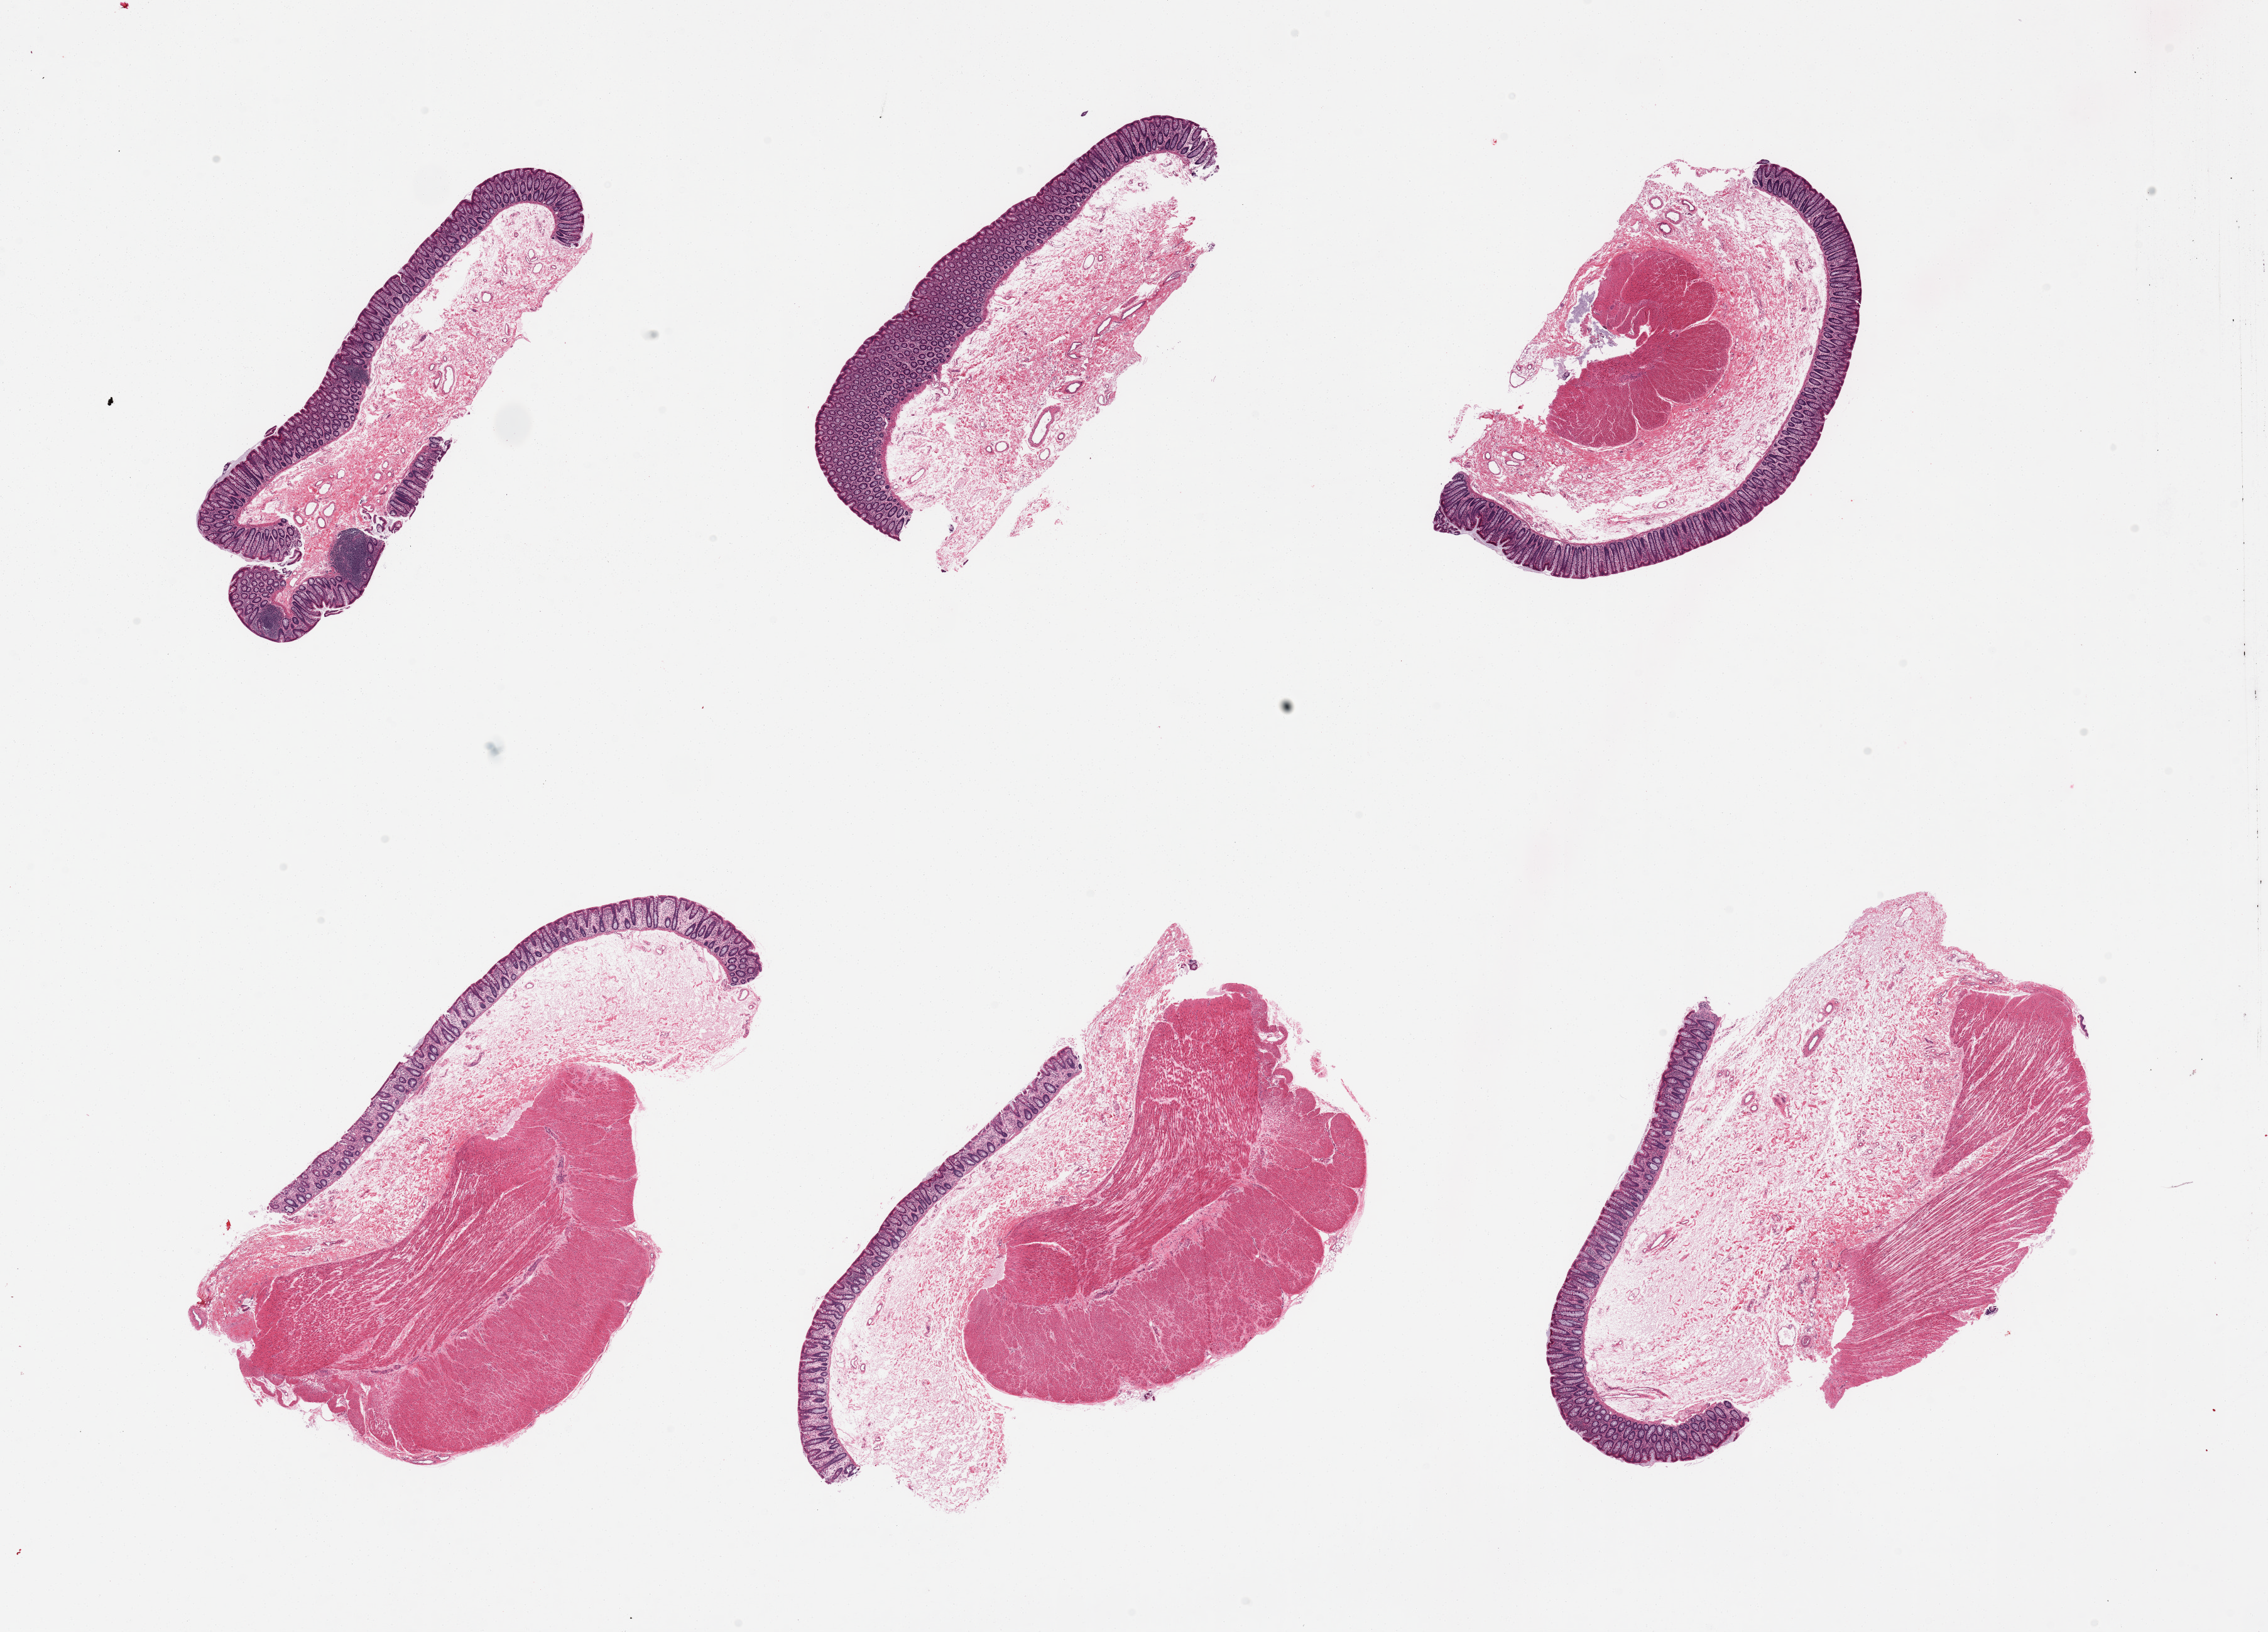
Digitized H&E-stained section, brightfield — low-resolution overview of the scanned area, about 28.5 x 20.5 mm (from a 20x scan). PAXgene-fixed, paraffin-embedded tissue. Target tissue: transverse colon. Tissue donor sample.
* pathologist's review note for this sample: 6 pieces; 2 without muscularis